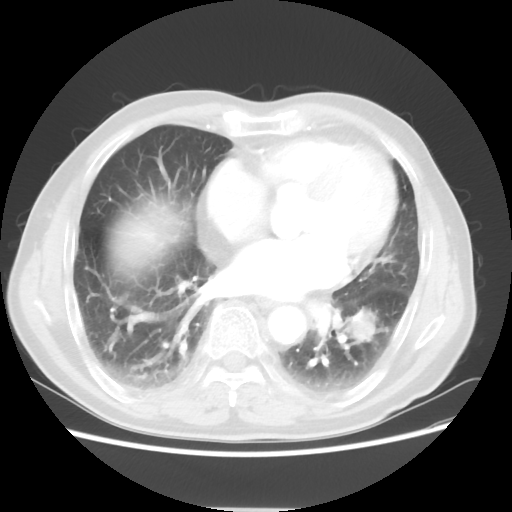
Chest CT, one axial slice; position 29 of 64 along the scan axis; 120 kVp; lung window (W 1500 / L -600 HU); 5 mm slice thickness; 512 × 512 image matrix, field of view 366 × 366 mm. Patient: male, 71 years. From the clinical record (not read from this slice): clinical TNM (as recorded): T1c N1 M0; histopathological grade: G2-3.
Annotated regions visible in this slice (bounding box drawn by a radiologist):
- lung tumour (recorded histology: adenocarcinoma): bounding box <340,302,385,353> (left, top, right, bottom; pixels)